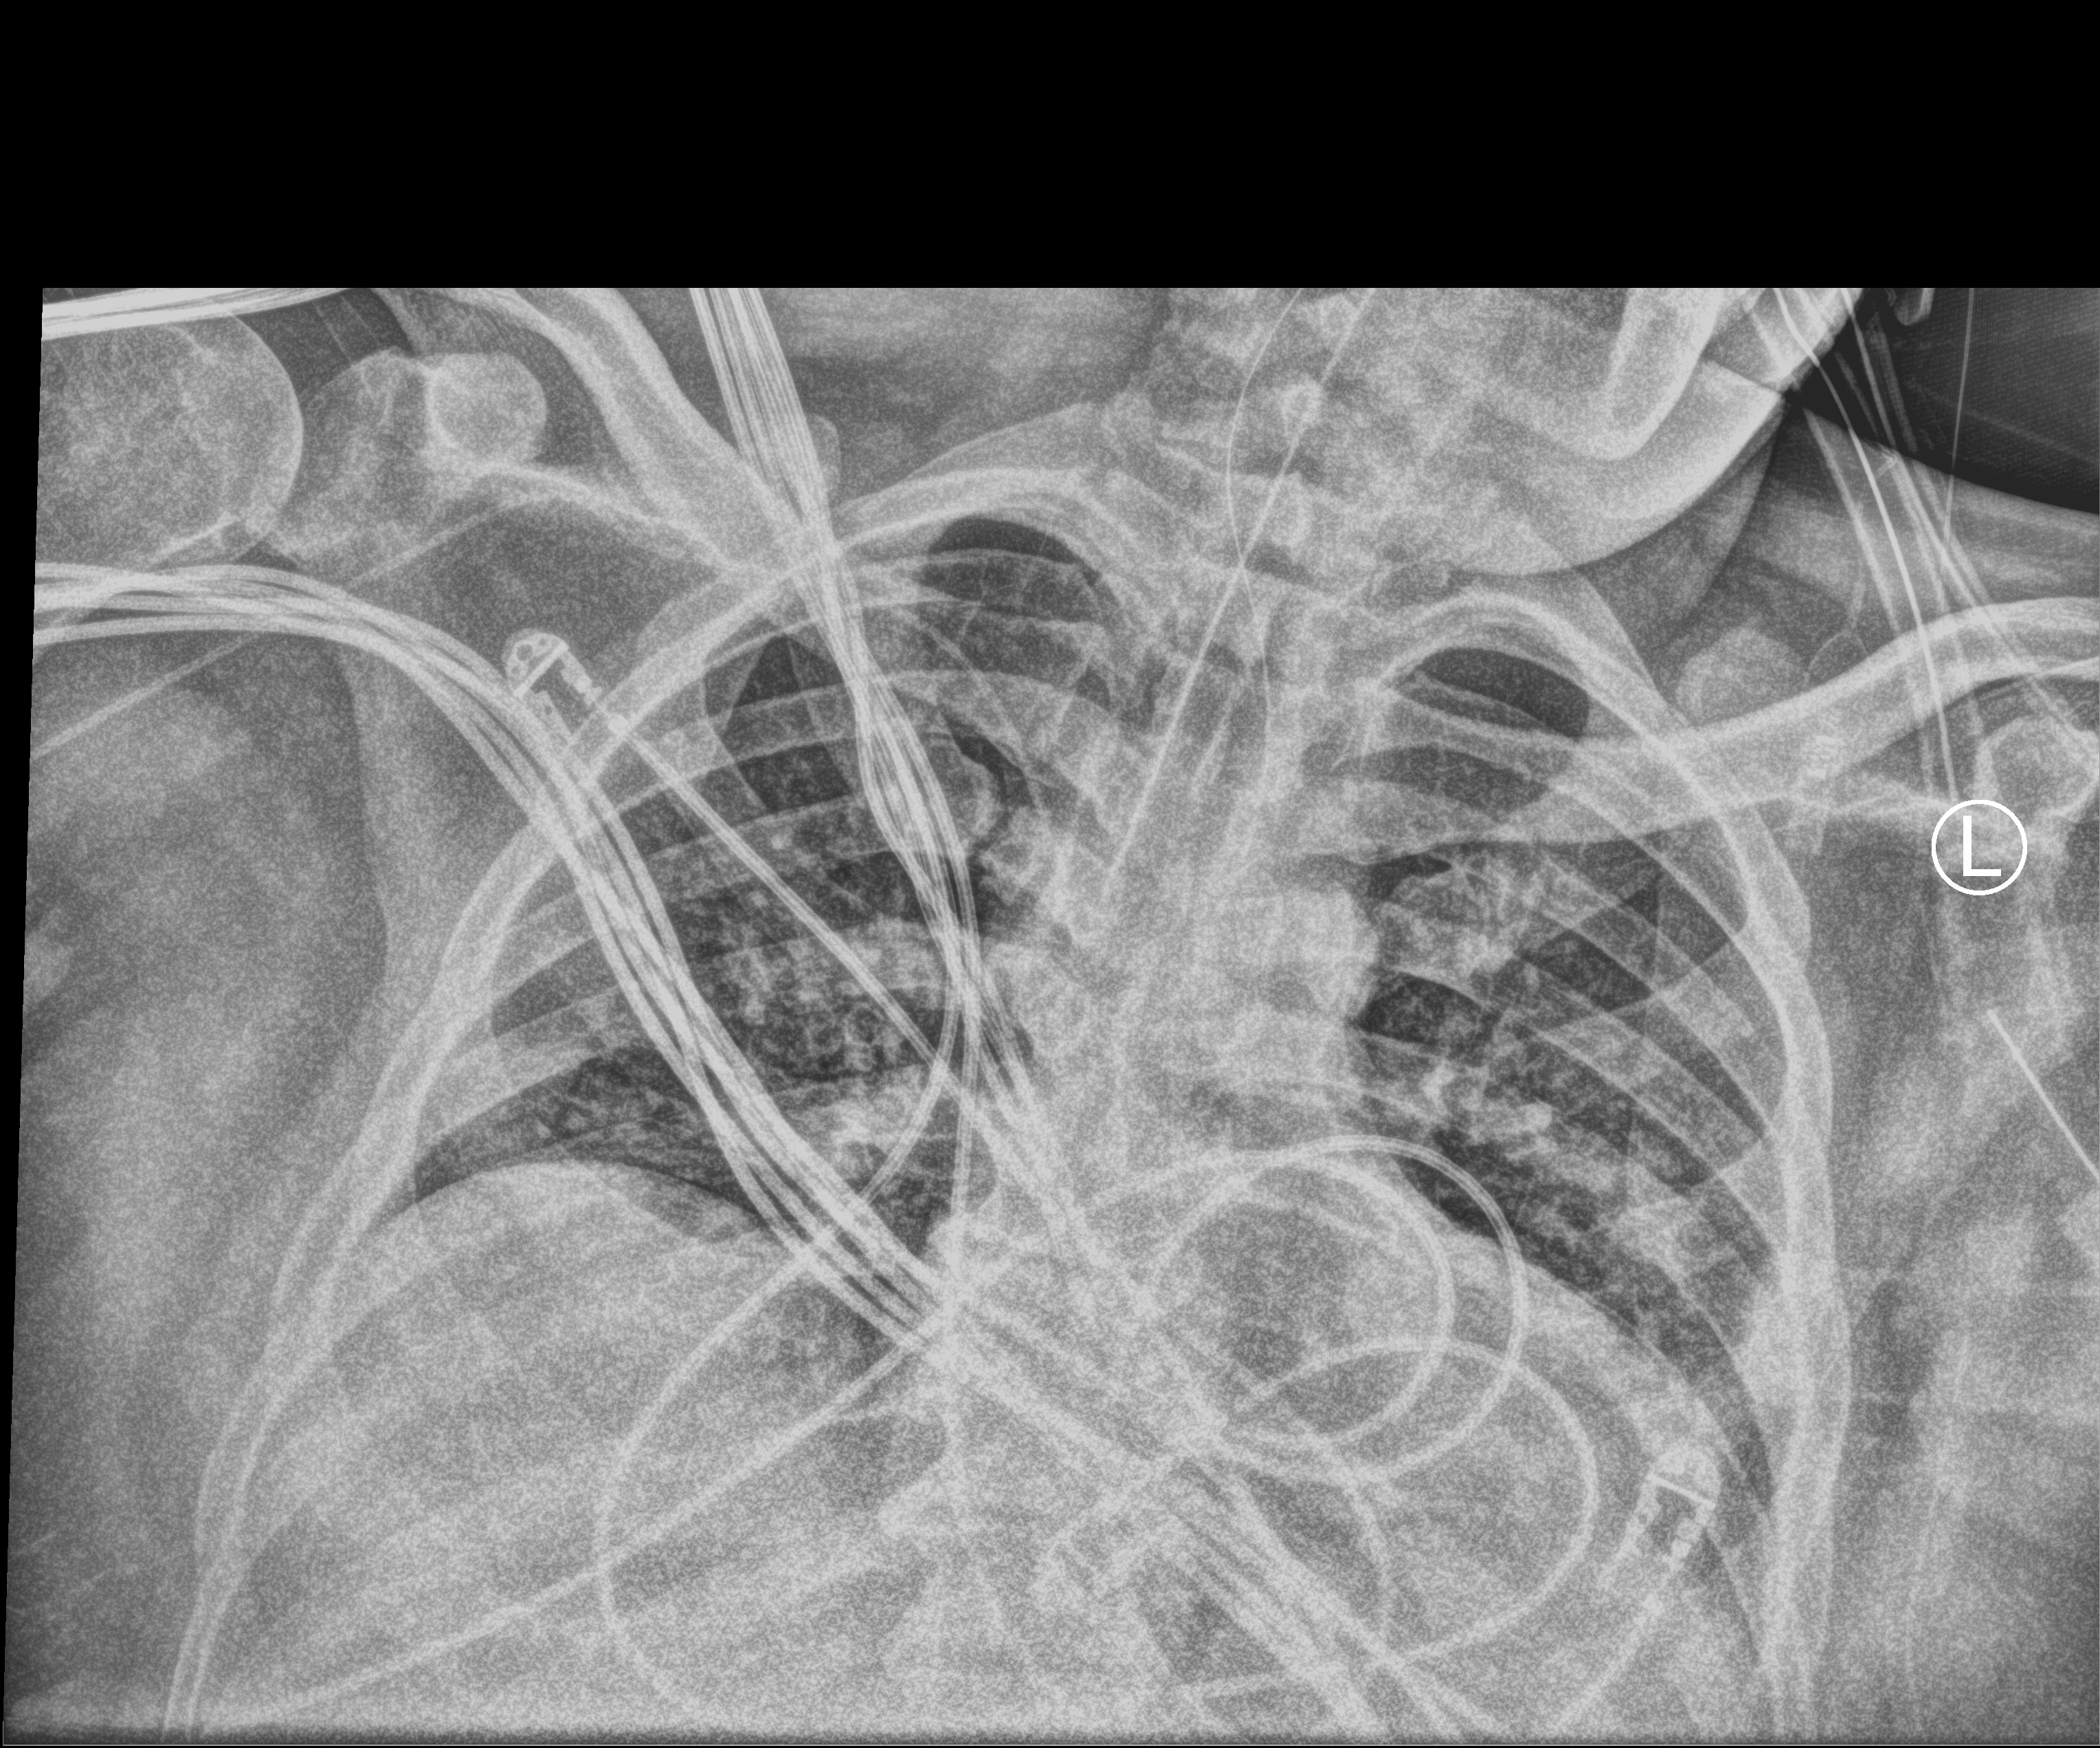
Bedside chest radiograph (computed radiography); anteroposterior (AP) projection. Patient hospitalised with COVID-19; male, aged 18–59 years.
Admission-level facts for this patient (not findings on this image; timing relative to this image not recorded): admitted to intensive care during this hospital stay: yes; length of hospital stay: 41 days.